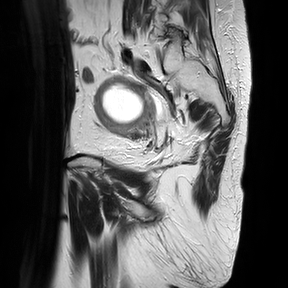
Pelvic MRI for cervical cancer, one sagittal slice. Slice 8 of 30 in the series (ordered by position). T2-weighted. 1.5 T. TE 100 ms, TR 4816.3 ms. 288 × 288 image matrix, field of view 300 × 300 mm. Female patient, age 74 years.
Structures marked on this image (manually delineated by an expert):
- uterus and cervix: bounding box <93,75,157,138> (left, top, right, bottom; pixels)